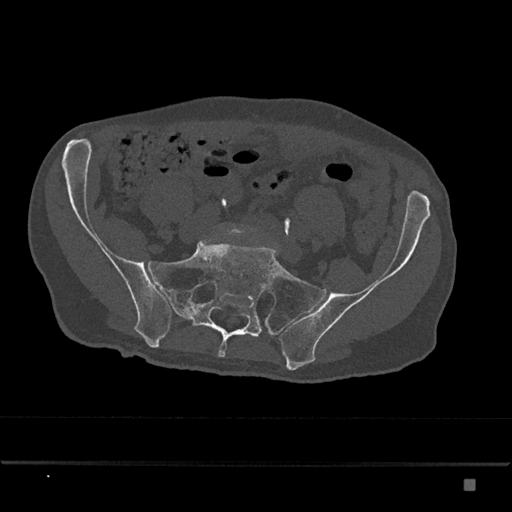
CT including the spine, one axial slice. Bone window (W 1800 / L 400 HU). 0.5 mm slice thickness. 512 × 512 image matrix. Patient: male, 72 years. Case-level facts recorded for this patient, not image findings: primary cancer: prostate.
Structures marked on this image (semi-automatically segmented with operator editing):
- L5 vertebra: bounding box [x1, y1, x2, y2] px = [222, 227, 252, 235]